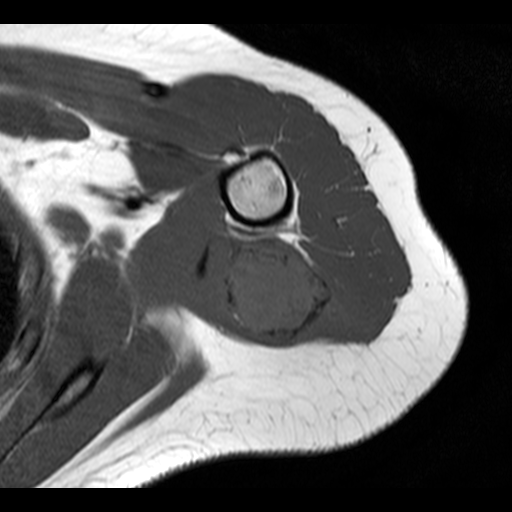
MRI of an extremity soft-tissue mass, one axial slice; slice 7 of 20 in the series (ordered by position); 4 mm slice thickness; 512 × 512 image matrix. Female patient. Case-level facts recorded for this patient, not image findings: histological type: malignant fibrous histiocytoma; grade: low; site of the primary tumour: left arm.
Structures marked on this image (manually delineated by an expert):
- gross tumour volume (mass): bounding box <220,241,340,346> (left, top, right, bottom; pixels)